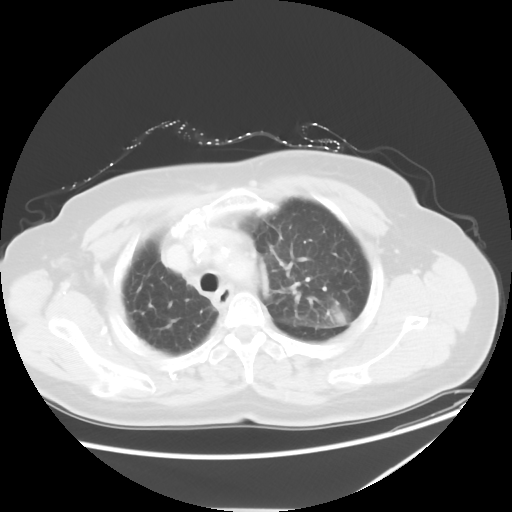
Chest CT, one axial slice; slice 43 of 54 in the series (ordered by position); reconstruction kernel STANDARD; 120 kVp; lung window (W 1500 / L -600 HU); 5 mm slice thickness; 512 × 512 image matrix, field of view 384 × 384 mm. Female patient, age 61 years. From the clinical record (not read from this slice): clinical TNM (as recorded): T1c N3 M1.
Structures marked on this image (bounding box drawn by a radiologist):
- lung tumour (recorded histology: adenocarcinoma): bounding box <310,300,354,332> (left, top, right, bottom; pixels)